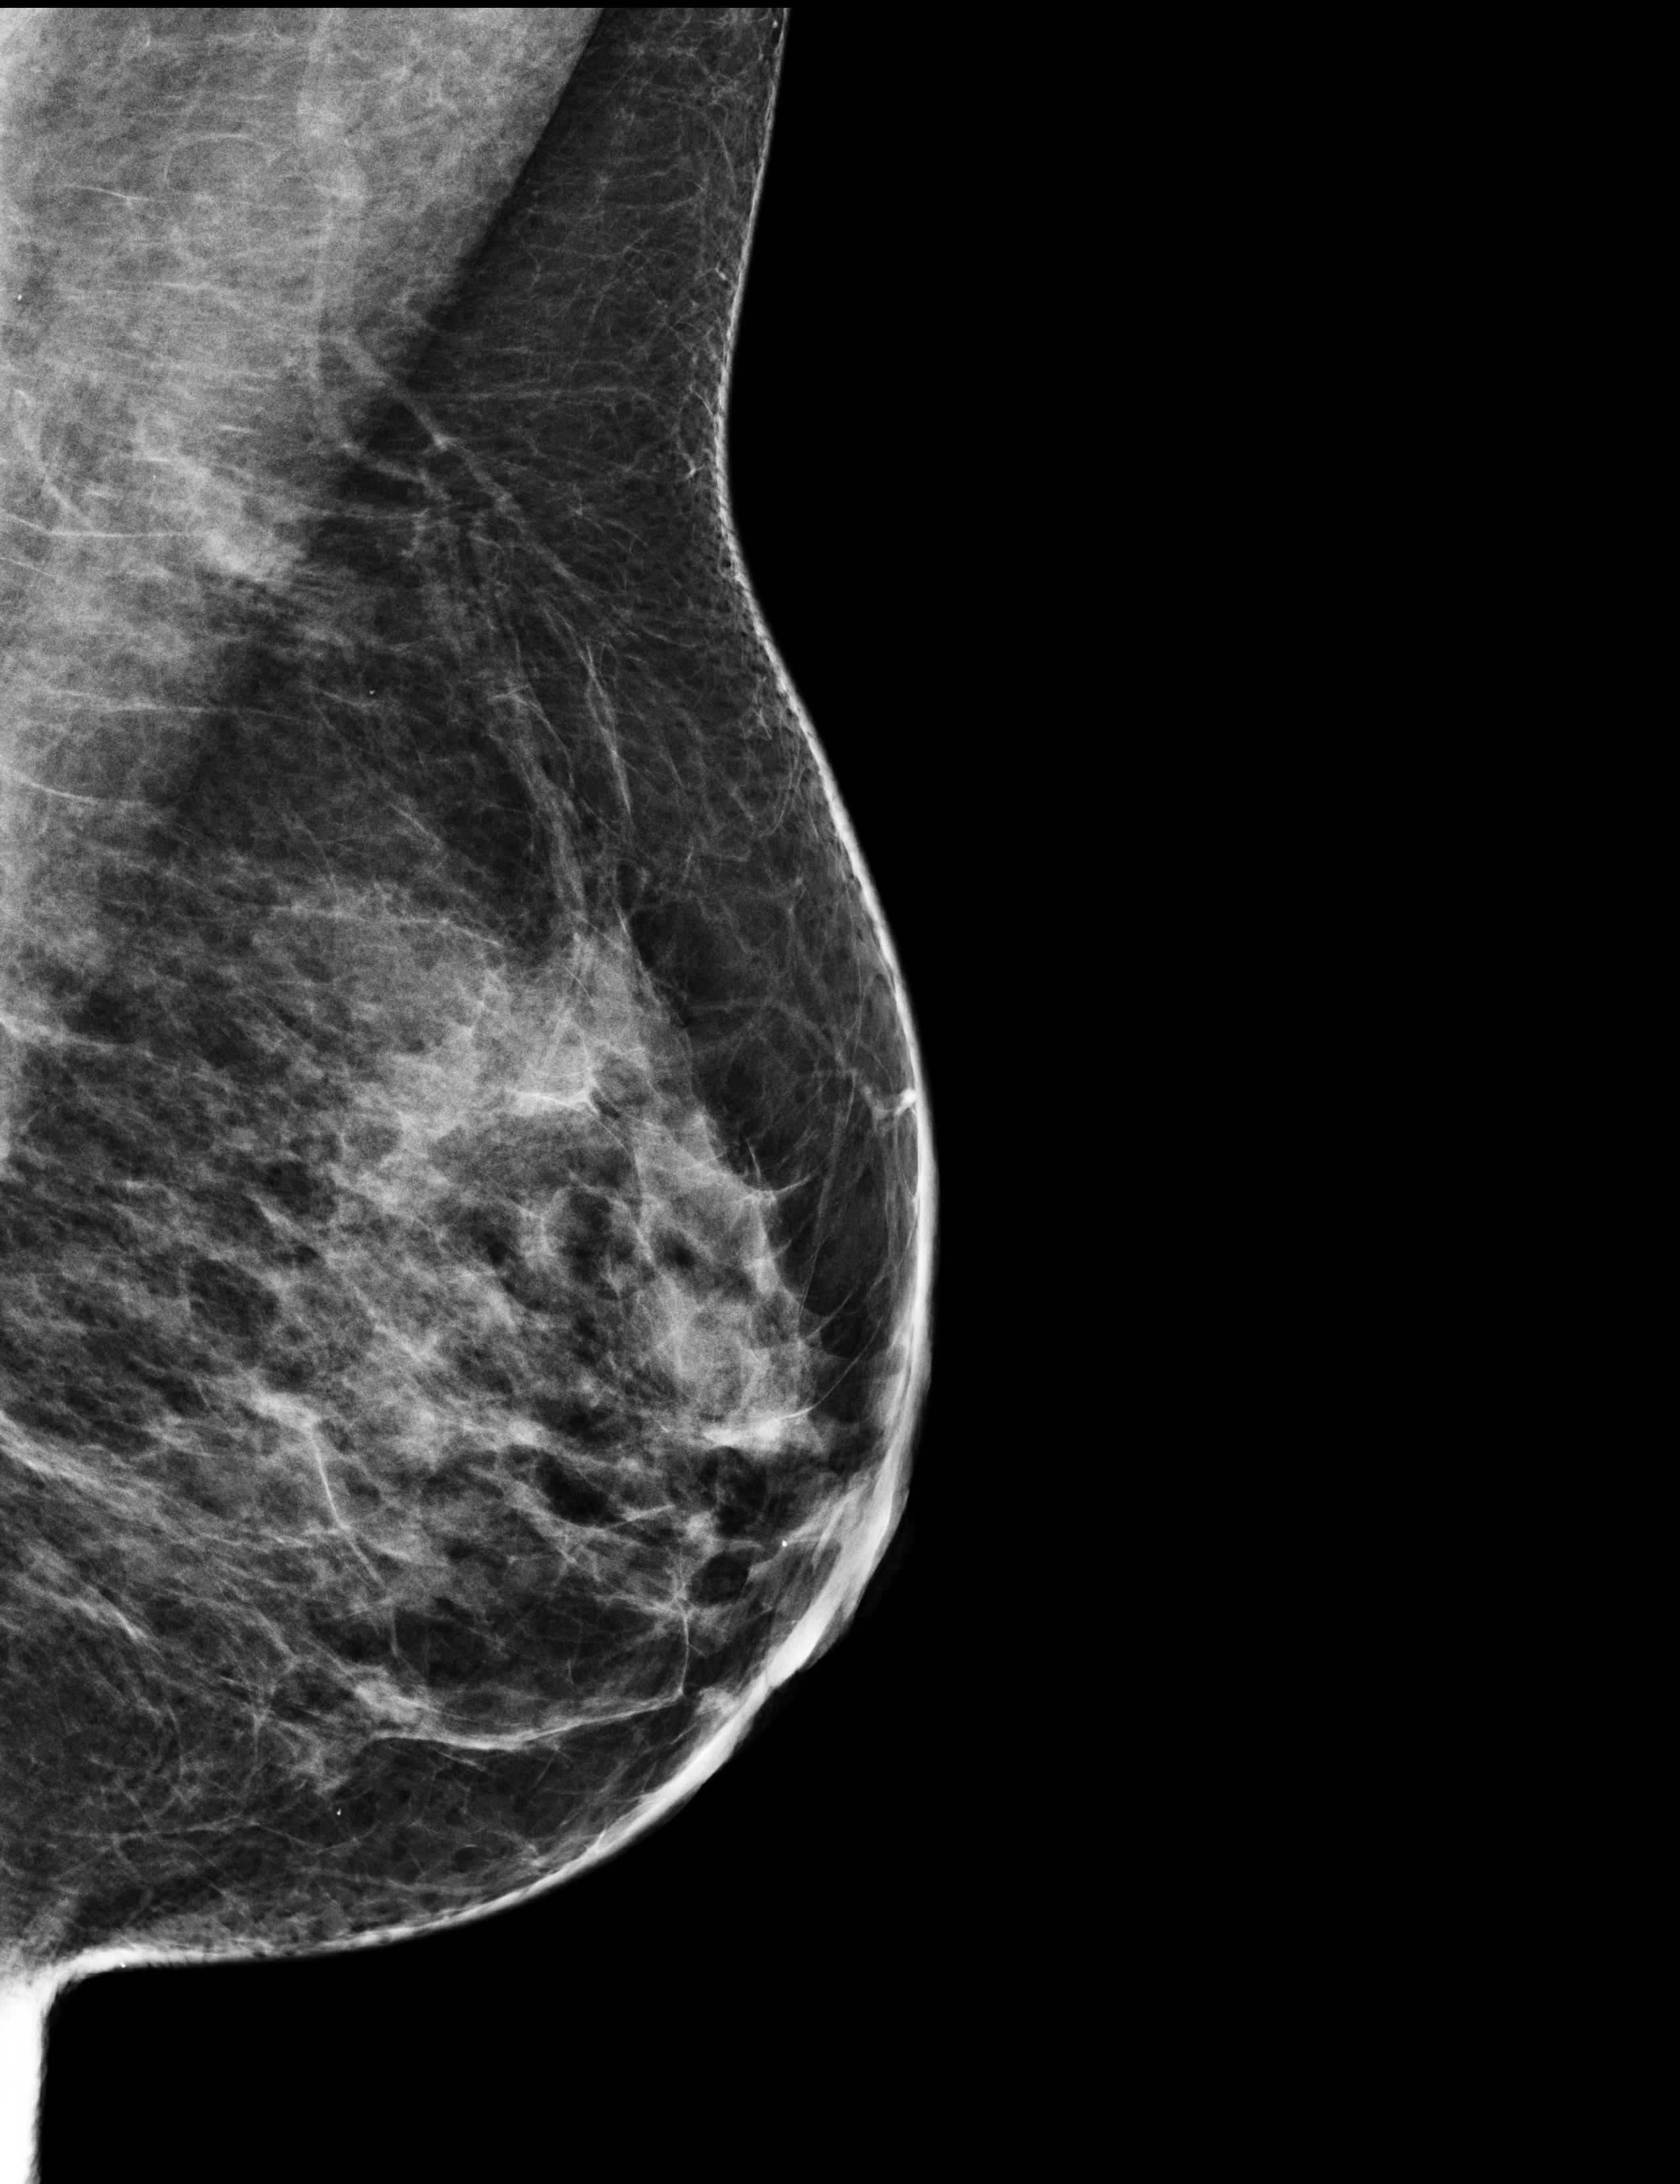
Full-field digital mammogram (FFDM); left breast; mediolateral oblique (MLO) view; annual screening mammography examination. Patient aged 46 years (female).
BI-RADS breast density category at the screening exam (both breasts, scale 1–4): 3. Final BI-RADS assessment for this screening round (tomosynthesis exam, both breasts): category 2. Recall: no recall after this screen.